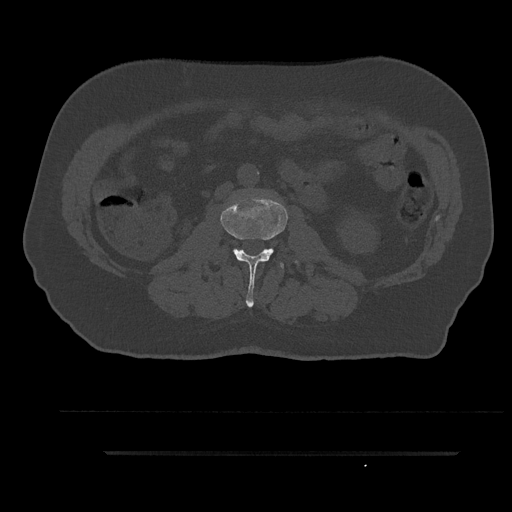
CT including the spine, one axial slice; position 95 of 797 along the scan axis; reconstruction kernel Br40s/3; 120 kVp; bone window (W 1800 / L 400 HU); 0.5 mm slice thickness; 512 × 512 image matrix, field of view 432 × 432 mm. Male patient, age 63 years. Case-level facts recorded for this patient, not image findings: primary cancer: renal.
Structures marked on this image (semi-automatically segmented with operator editing):
- L2 vertebra: bounding box [x1, y1, x2, y2] px = [221, 197, 297, 308]